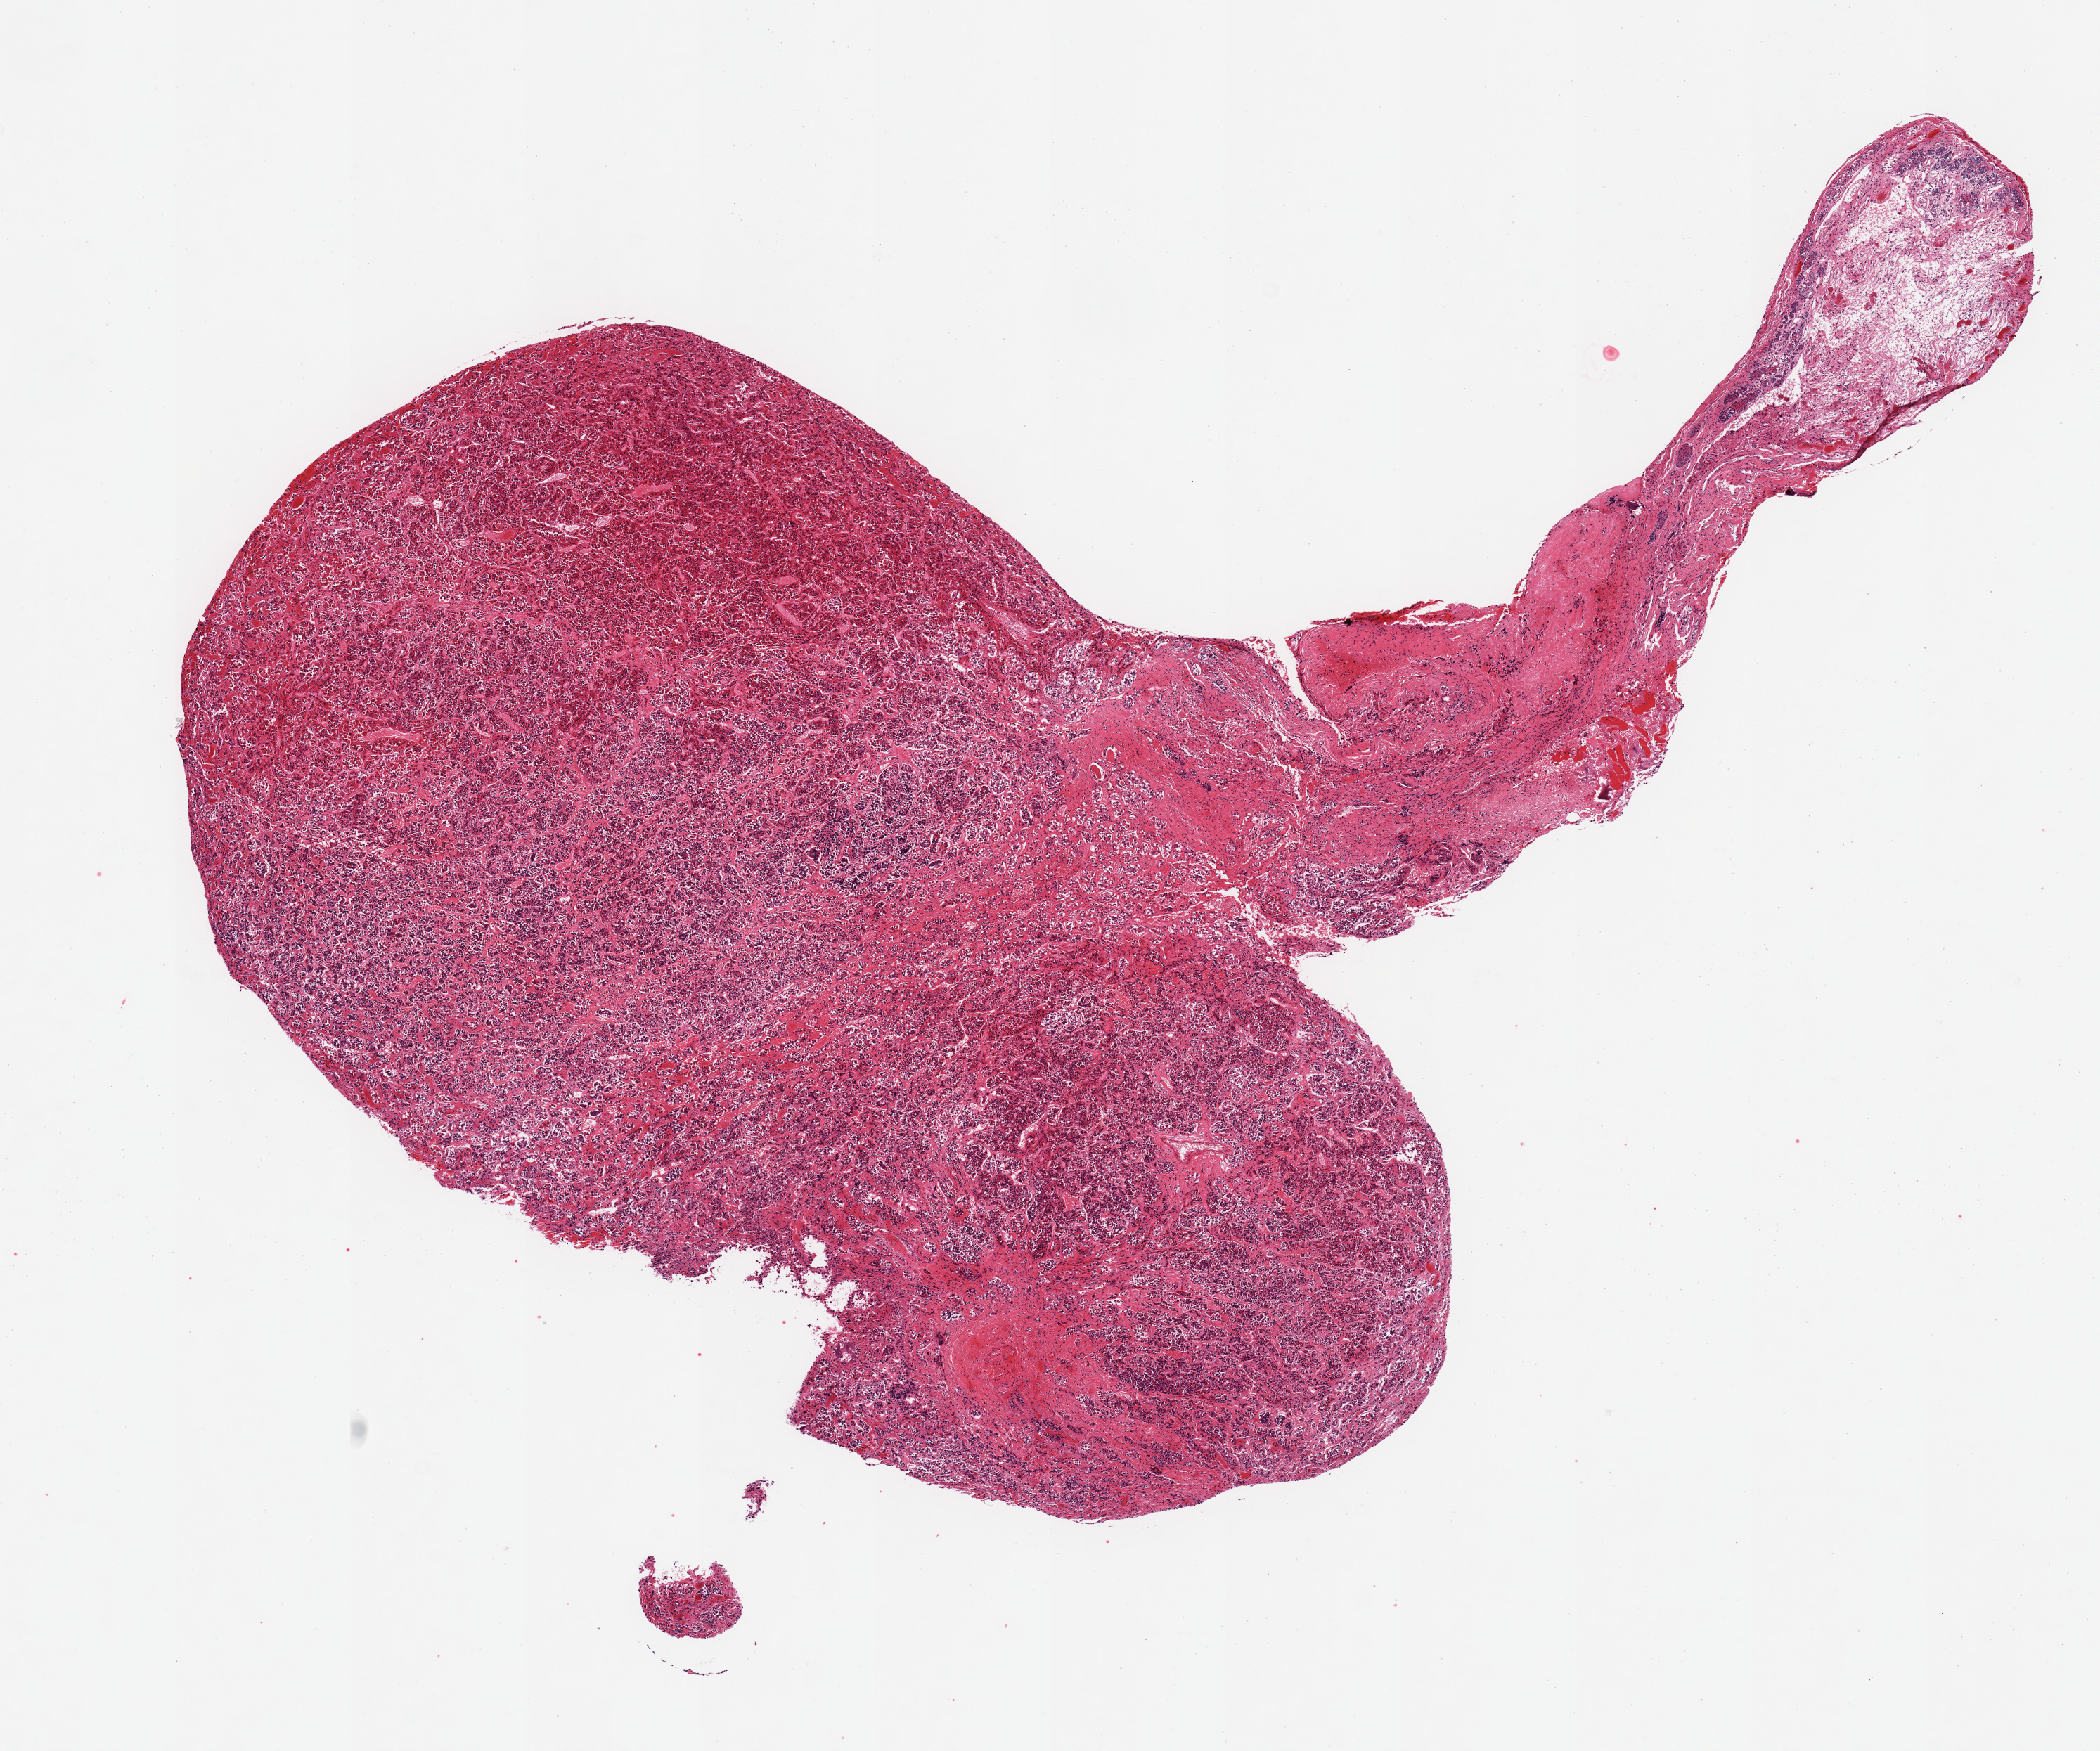
H&E whole-slide image, a low-resolution overview of the entire scanned area, about 11.8 x 9.9 mm (from a 20x scan). PAXgene-fixed paraffin-embedded (PFPE) section. Target tissue: pituitary. Donor tissue sample. Donor sex: male.
Review note (as recorded): 1 pieces, mainly adenohypophysis; trace nubbin (~1mm) neurohypophysis.